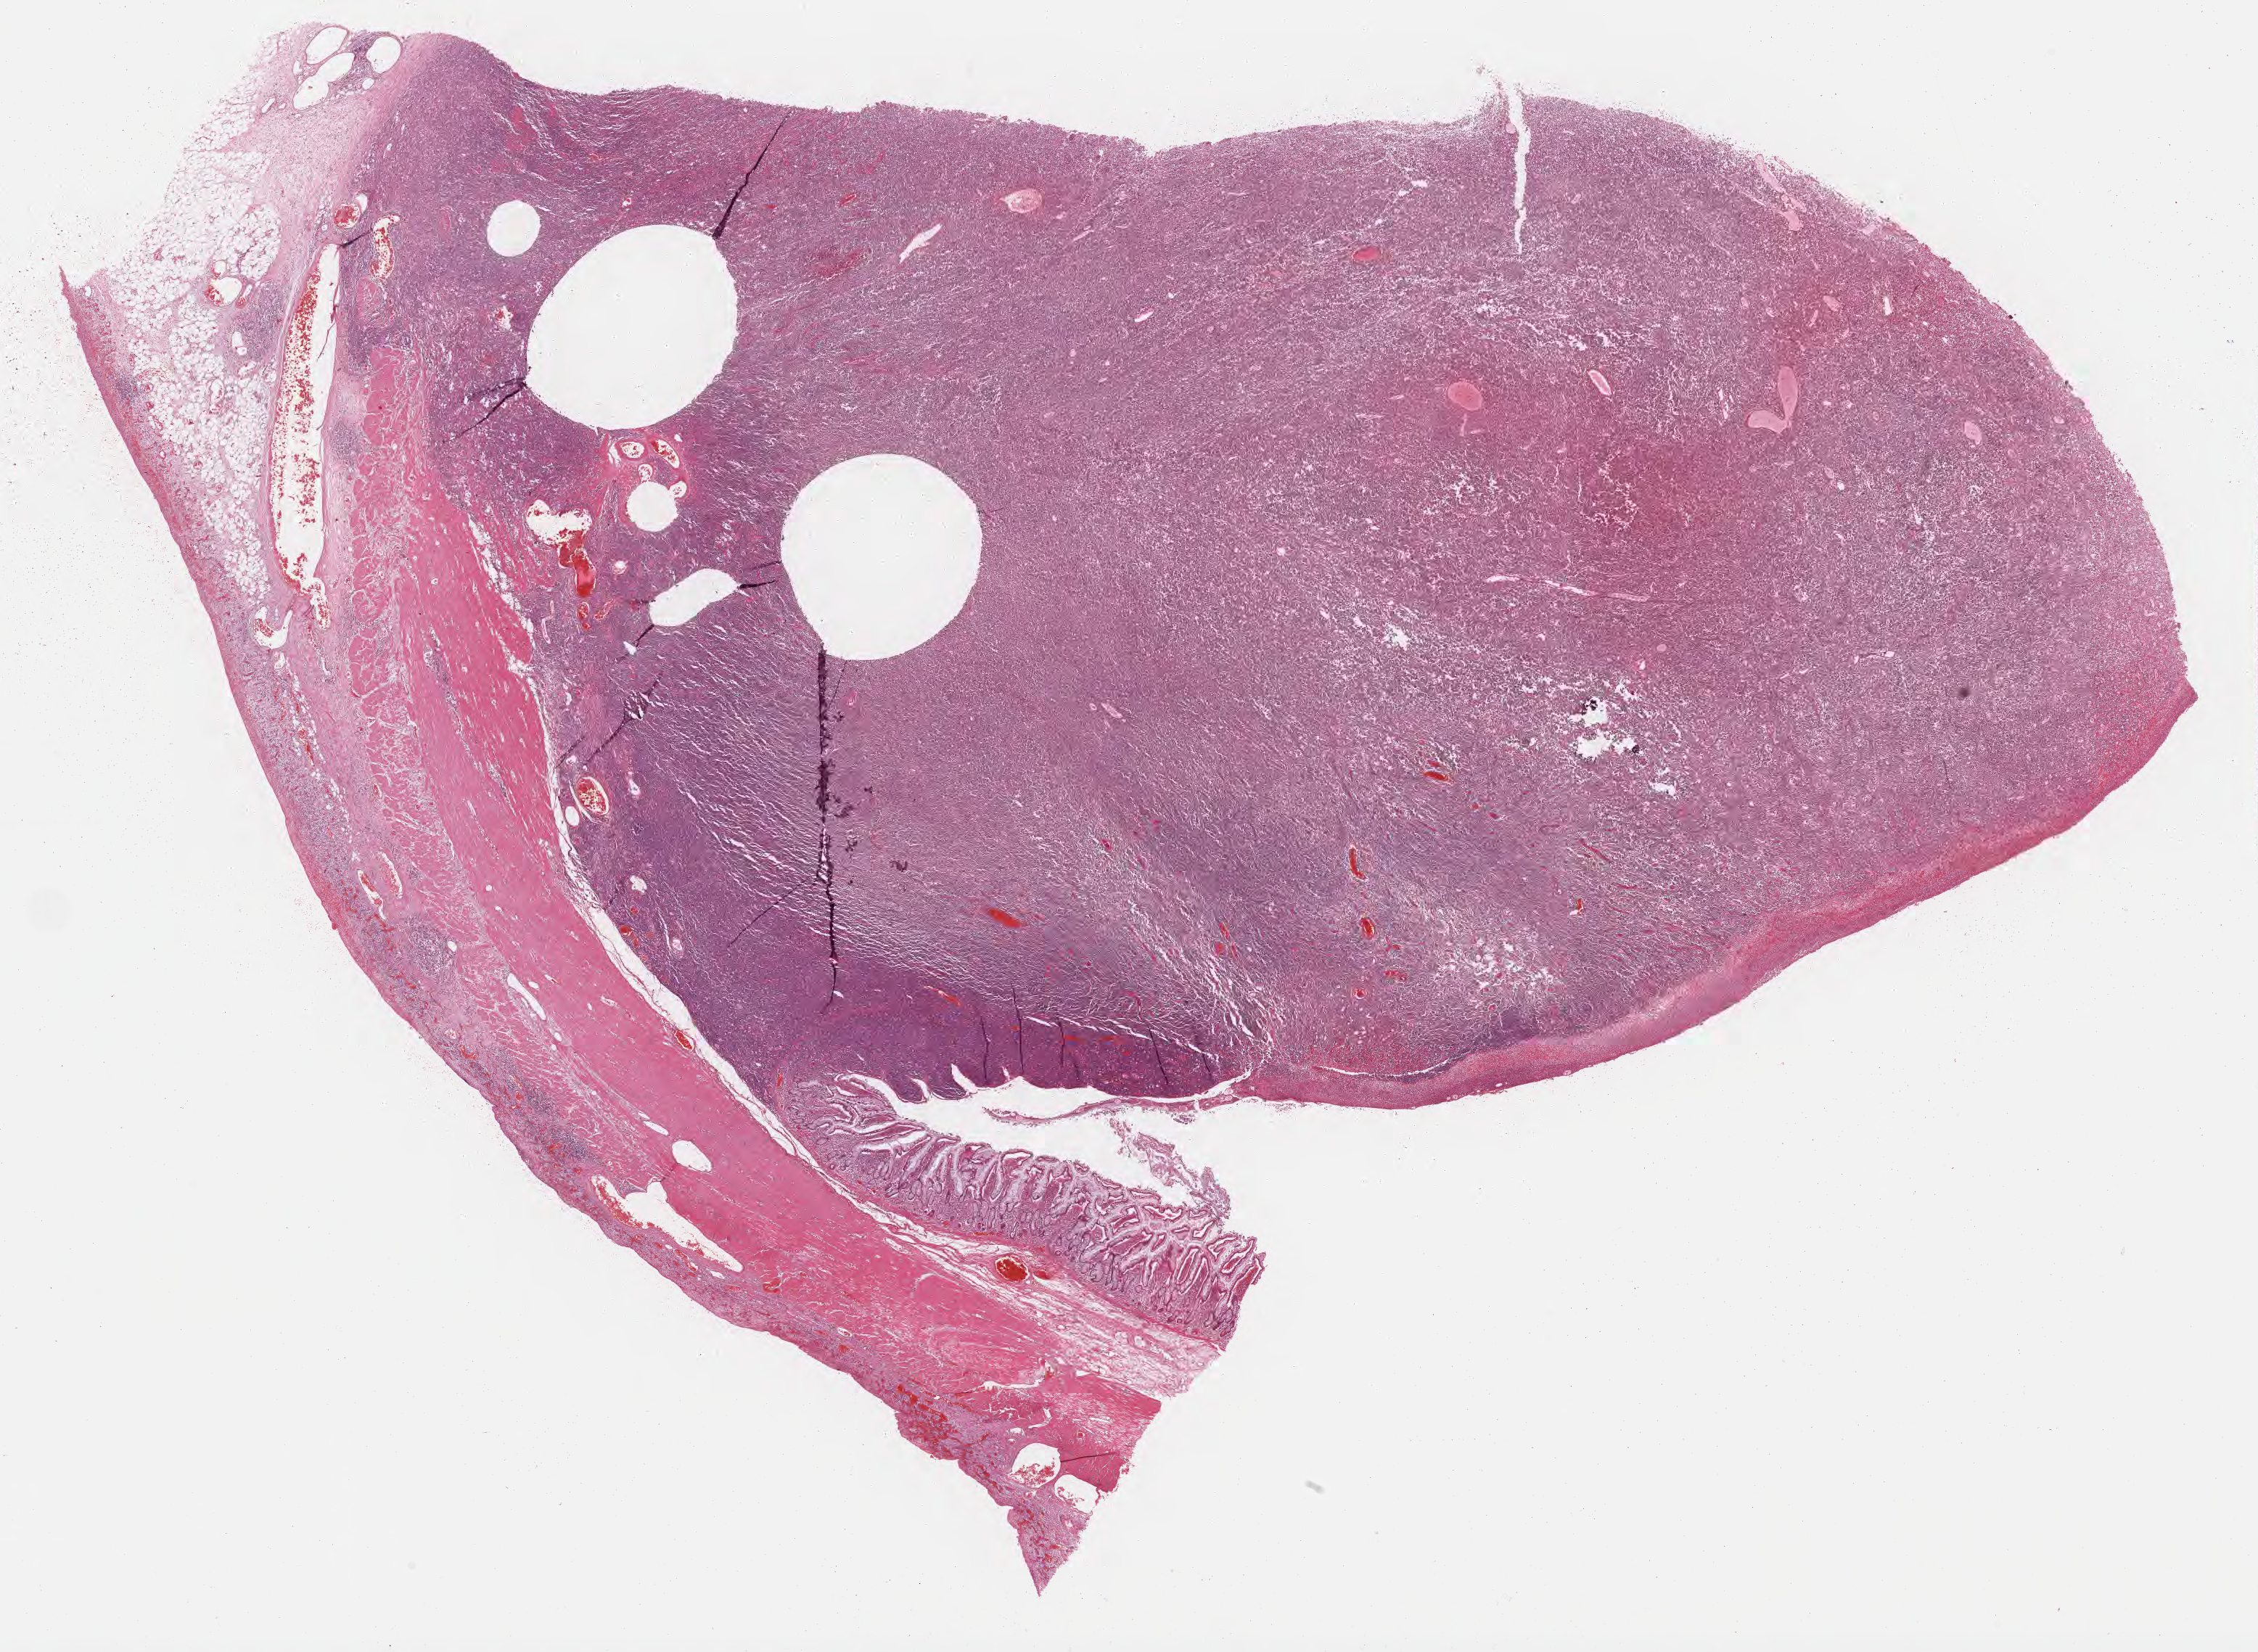
H&E whole-slide image — low-resolution overview of the scanned area, about 25.2 x 18.4 mm; FFPE section; specimen: primary tumor. Female patient, age 15 years. Slide review estimates, as recorded: tumor cells 75%, tumor nuclei 90%, stromal cells 10%, necrosis 0%, normal cells 15%. Infiltration values recorded for this section: lymphocyte infiltration 70%, monocyte infiltration 15%, neutrophil infiltration 0%.
• Ann Arbor stage (patient): Stage IV
• histologic diagnosis: Burkitt lymphoma, NOS
• section: bottom of the tissue portion